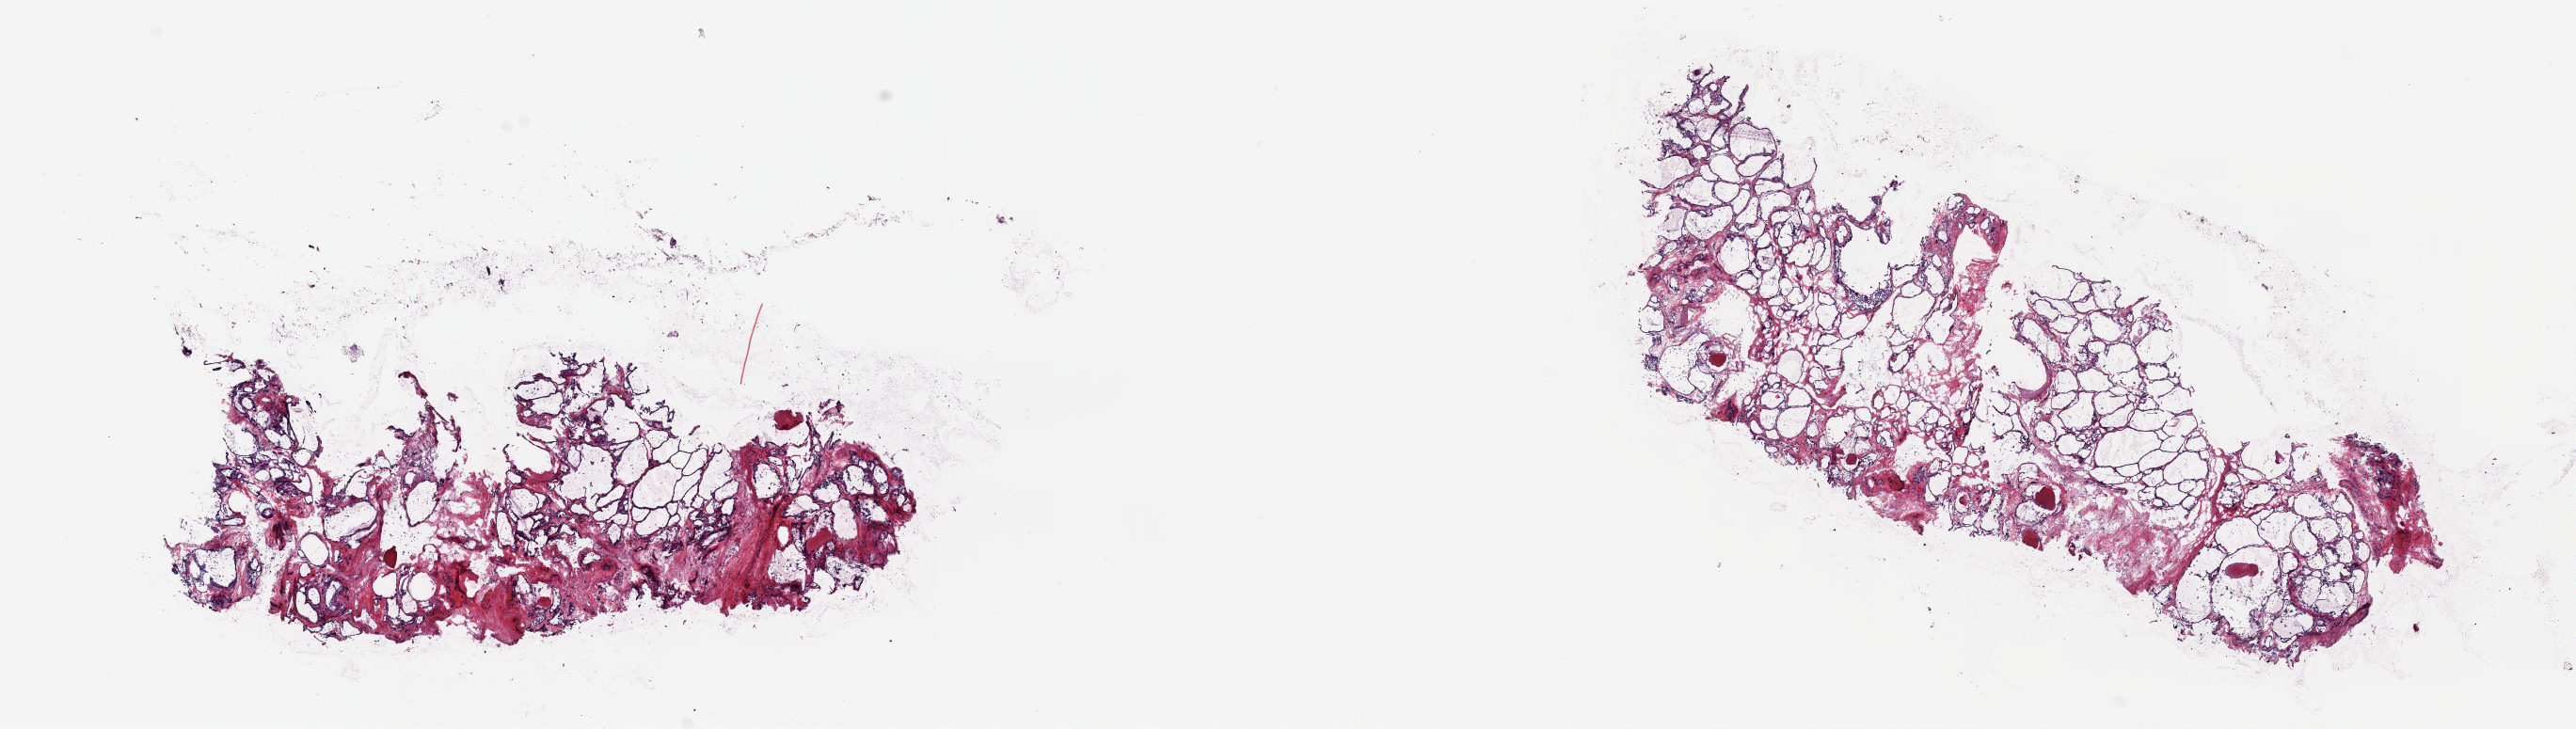
Hematoxylin and eosin (H&E) stained whole-slide image — a low-resolution overview of the entire scanned area, about 21.6 x 6.1 mm (slide scanned at 20x). Frozen section from the top of the tissue portion. Thyroid, solid tissue normal (non-tumour tissue) sample. Female, age 28 years at initial diagnosis. Slide review estimates, as recorded: tumour cells 0%, tumour nuclei 0%, normal cells 80%, stromal cells 20%, necrosis 0%. Infiltration values recorded for this section: lymphocyte infiltration 2%, monocyte infiltration 2%, neutrophil infiltration 0%.
This section: solid tissue normal sample (biorepository sample class). Patient diagnosis: Papillary adenocarcinoma, NOS (thyroid gland).